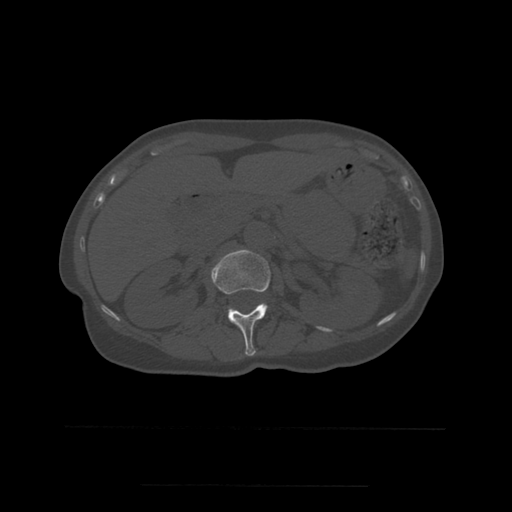
CT including the spine, one axial slice; position 230 of 544 along the scan axis; bone window (W 1800 / L 400 HU); 512 × 512 image matrix, field of view 350 × 350 mm. Patient age 58 years. From the clinical record (not read from this slice): primary cancer: lung.
Annotated regions visible in this slice (semi-automatically segmented with operator editing):
- L1 vertebra: bounding box (x1, y1, x2, y2) in pixels: (211, 250, 271, 356)